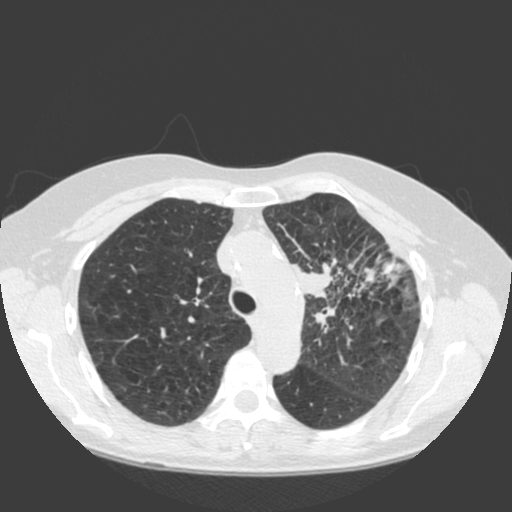
Low-dose screening chest CT, one axial slice. Position 139 of 184 along the scan axis. 120 kVp. Lung window (W 1500 / L -600 HU). 512 × 512 image matrix.
Annotated regions visible in this slice (outlined manually by an expert reader):
- lesion 1 (tumor, hilum of left lung): bounding box [x1, y1, x2, y2] px = [294, 263, 332, 297]